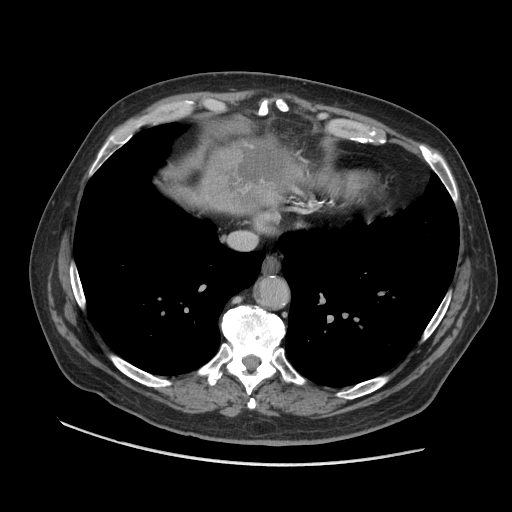
Contrast-enhanced abdominal CT (liver protocol), one axial slice. Slice 94 of 109 in the series (ordered by position). Reconstruction kernel STANDARD. Soft-tissue window (W 400 / L 40 HU). 512 × 512 image matrix, field of view 420 × 420 mm. Case-level facts recorded for this patient, not image findings: diagnosis: hepatocellular carcinoma (patient treated with transarterial chemoembolisation; whether this scan precedes or follows treatment is not stated here); TNM stage (as recorded): Stage-I; Child-Pugh class: A; tumour nodularity: uninodular.
Structures marked on this image (semi-automatic segmentation, software-assisted and operator-edited):
- liver parenchyma outside the tumour (the mass and vessels are separate outlines, so this box may not span the whole liver): bounding box <176,162,278,214> (left, top, right, bottom; pixels)
- mass: <198,135,302,218>